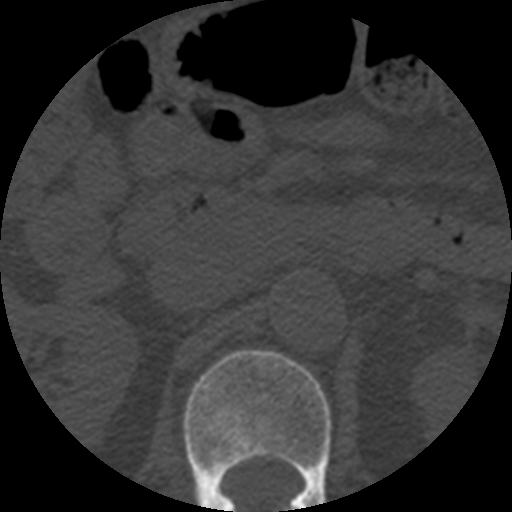
CT including the spine, one axial slice. Position 191 of 508 along the scan axis. Bone window (W 1800 / L 400 HU). 1.25 mm slice thickness. 512 × 512 image matrix, field of view 160 × 160 mm. Patient age 57 years. Case-level facts recorded for this patient, not image findings: primary cancer: prostate.
Outlined on this slice (semi-automatic segmentation, software-assisted and operator-edited):
- L1 vertebra: bounding box [x1, y1, x2, y2] px = [183, 350, 332, 512]